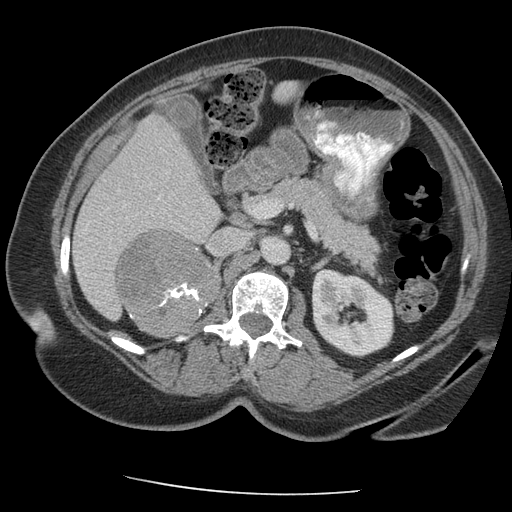
Contrast-enhanced abdominal CT, one axial slice. Slice 118 of 163 in the series (ordered by position). Reconstruction kernel STANDARD. 140 kVp. Intravenous contrast given. Soft-tissue window (W 400 / L 40 HU). 512 × 512 image matrix. Female patient, age 70 years. Case-level facts recorded for this patient, not image findings: diagnosis: adrenocortical carcinoma; tumour side: right adrenal; tumour size at pathology: 9.5 cm; Ki-67 index: 5 %; stage (as recorded): 2.
Structures marked on this image (semi-automatic segmentation, software-assisted and operator-edited):
- mass: box from (x=118, y=230) to (x=218, y=335) px